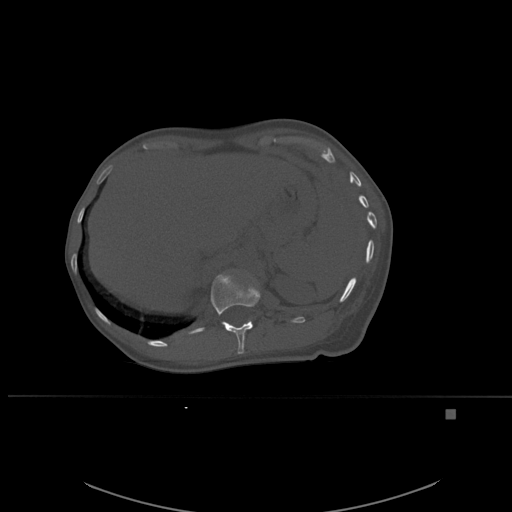
CT including the spine, one axial slice. Slice 276 of 537 in the series (ordered by position). Bone window (W 1800 / L 400 HU). 512 × 512 image matrix. Patient: female, 45 years. Case-level facts recorded for this patient, not image findings: primary cancer: lung.
Structures marked on this image (semi-automatic segmentation, software-assisted and operator-edited):
- T12 vertebra: bounding box [x1, y1, x2, y2] px = [210, 272, 260, 354]